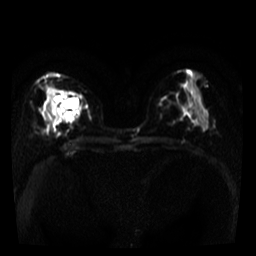
Breast MRI, one axial slice. Slice 19 of 39 in the series (ordered by position). Diffusion-weighted series; image 2 of 4 stored at this slice position (different b-values; order by instance number). 3 T. 256 × 256 image matrix, field of view 280 × 280 mm. Female patient.
Structures marked on this image (outlined manually by an expert reader):
- tumour on diffusion-weighted imaging: box from (x=47, y=92) to (x=85, y=114) px